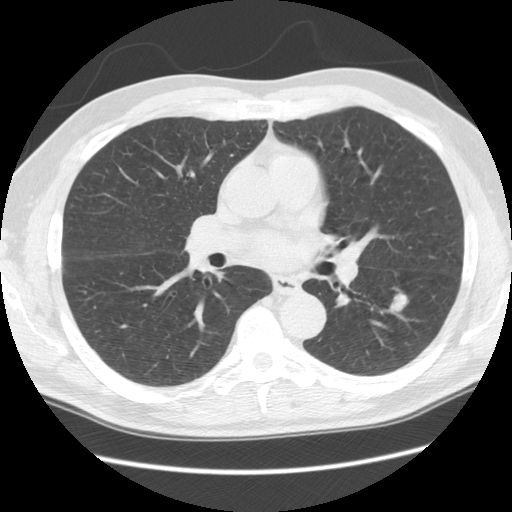
Low-dose screening chest CT, axial slice, third screening round (two years after baseline), lung window (W 1500 / L -600 HU), 2.5 mm slice thickness, standard (soft-tissue) reconstruction kernel (STANDARD), 512 × 512 image matrix. Male participant, aged 60 years at enrolment. Current smoker at enrolment.
Lesion marked by an expert reader, box from (x=382, y=289) to (x=417, y=319) px. The screening reader recorded 5 non-calcified nodules or masses ≥4 mm on this exam (left lower lobe, right lower lobe, right lower lobe, left lower lobe, left upper lobe); which of them this box marks is not recorded. Participant outcome: lung cancer diagnosed 153 days after this screen — large cell neuroendocrine carcinoma, left lower lobe, poorly differentiated (G3), stage IB (AJCC 6th edition), 33 mm at pathology.